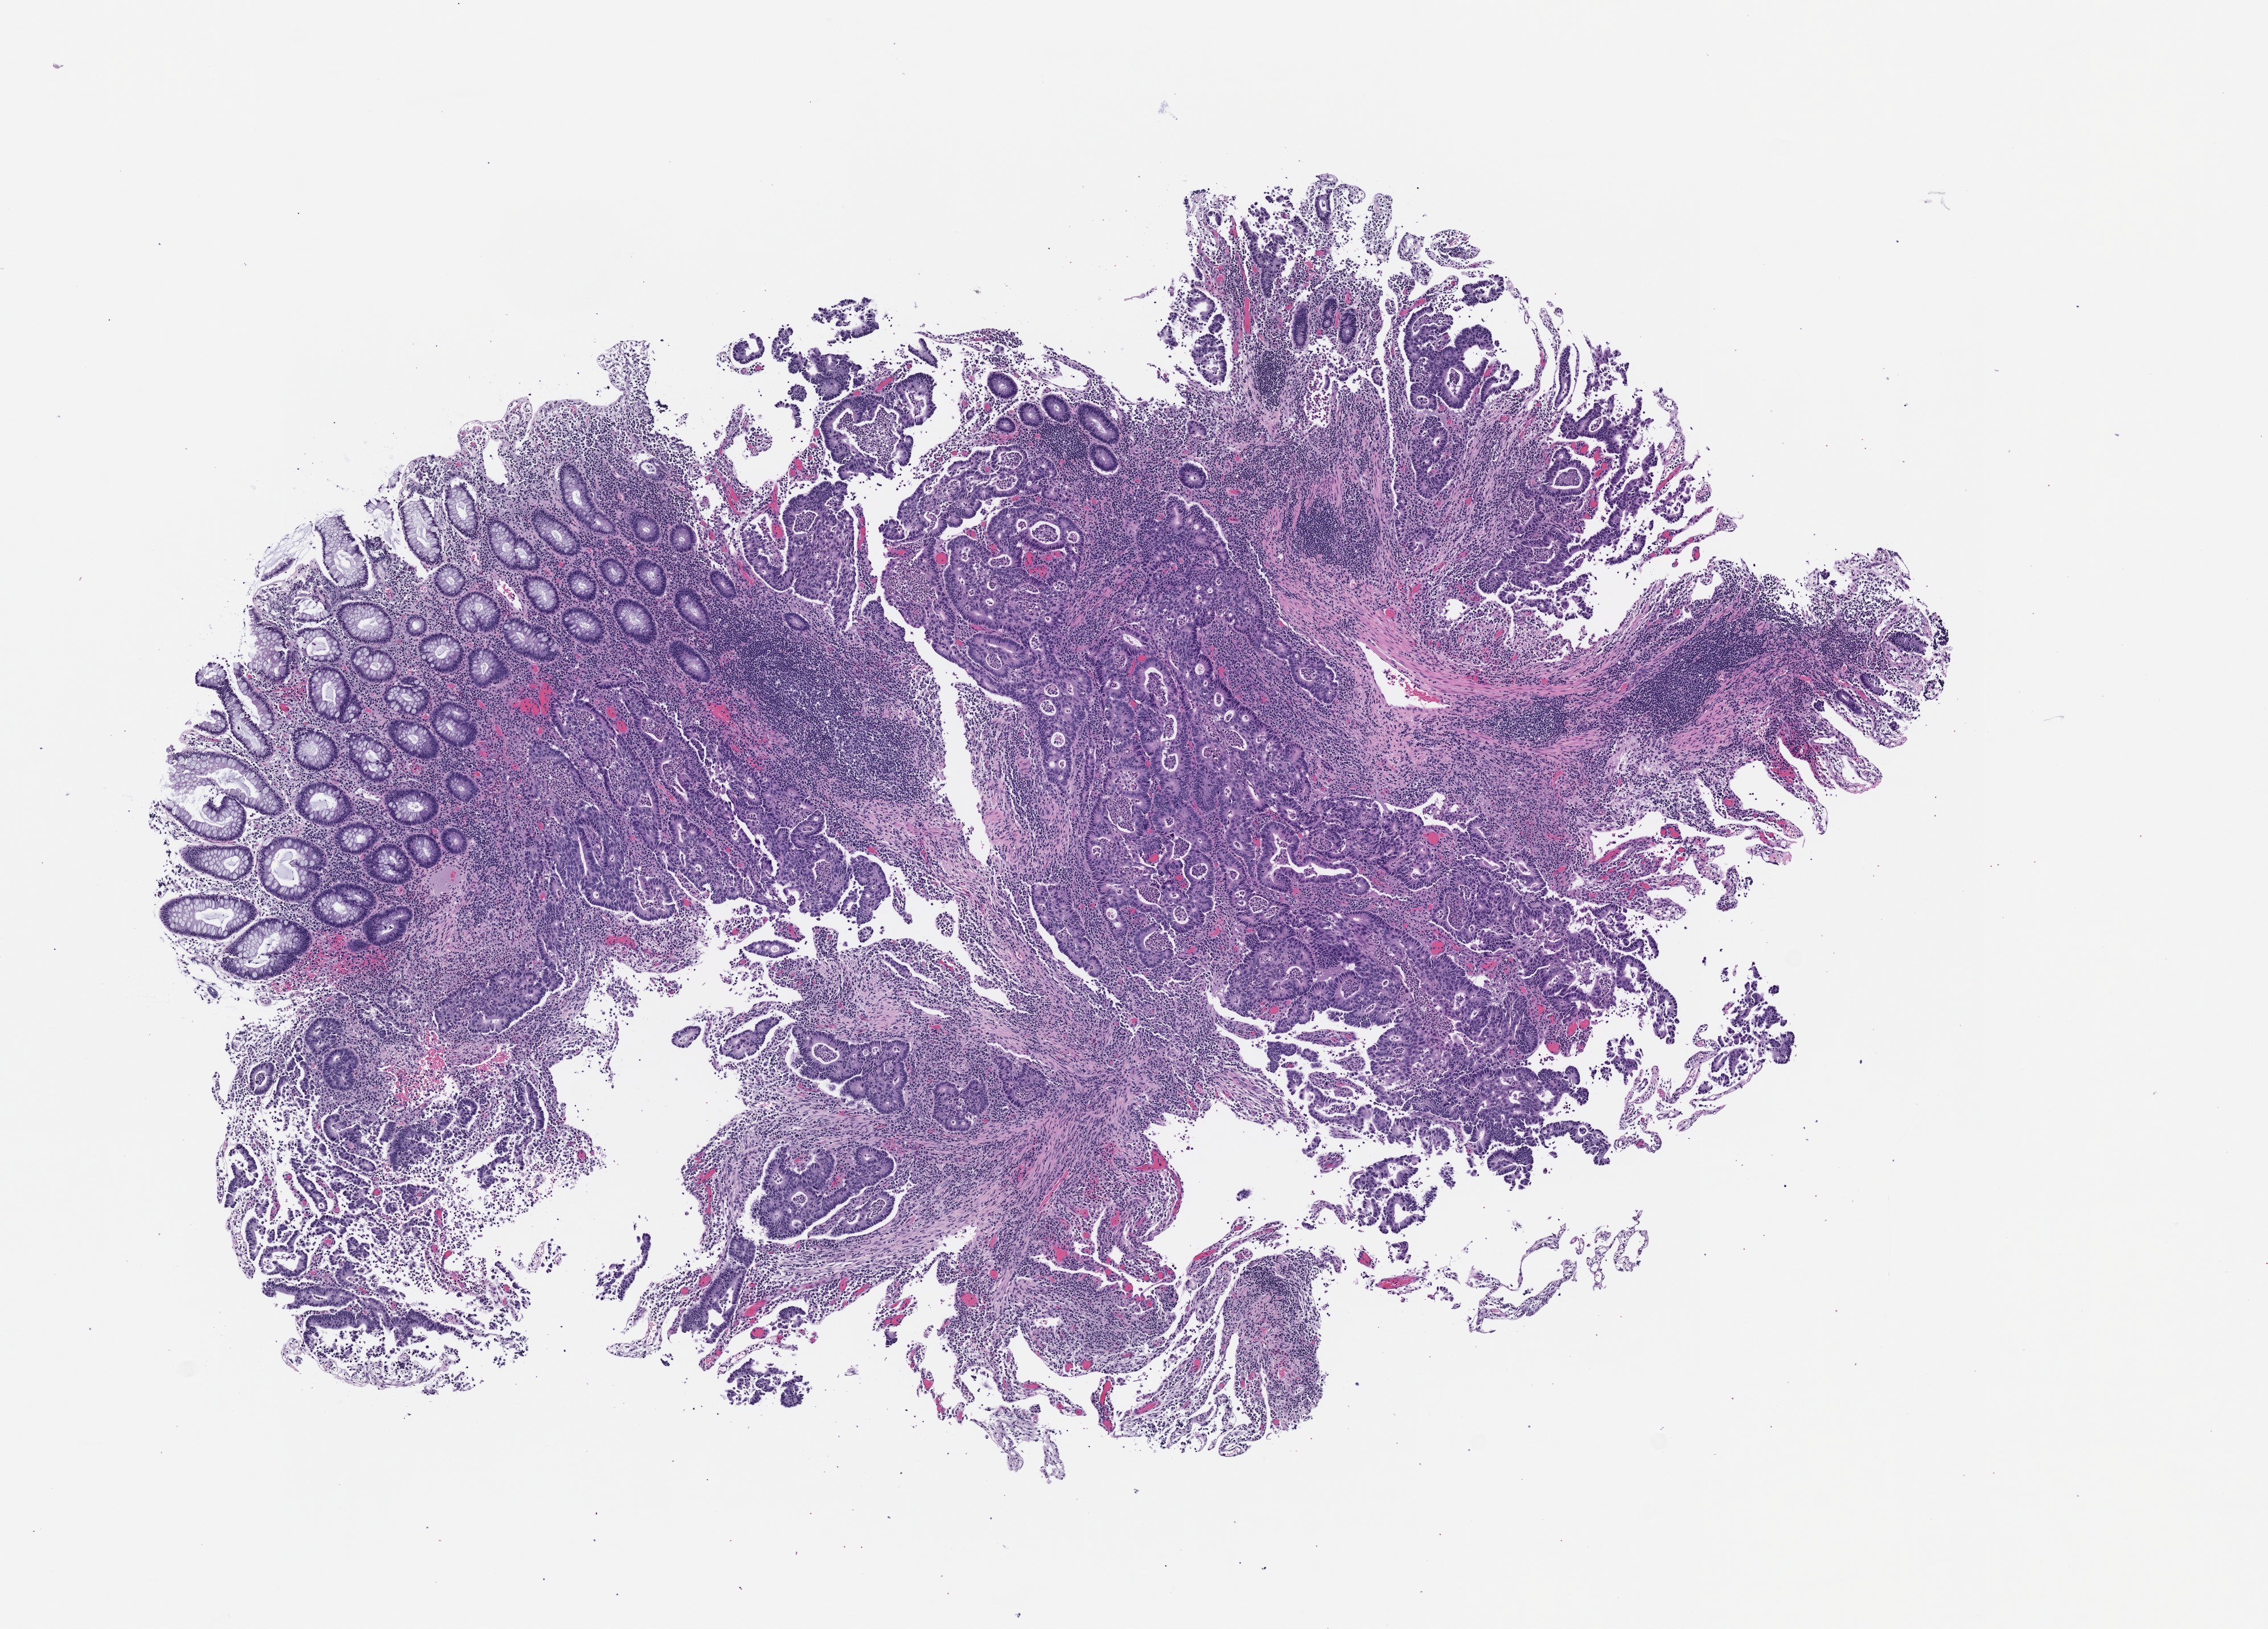
Digitized haematoxylin and eosin-stained section of the patient's (originator) tumor tissue — a low-resolution overview of the entire scanned area, about 8.0 x 5.8 mm; formalin-fixed, paraffin-embedded (FFPE) tissue; originating tumor site category: colon. Patient: male.
Diagnosis: Colon Adenocarcinoma.